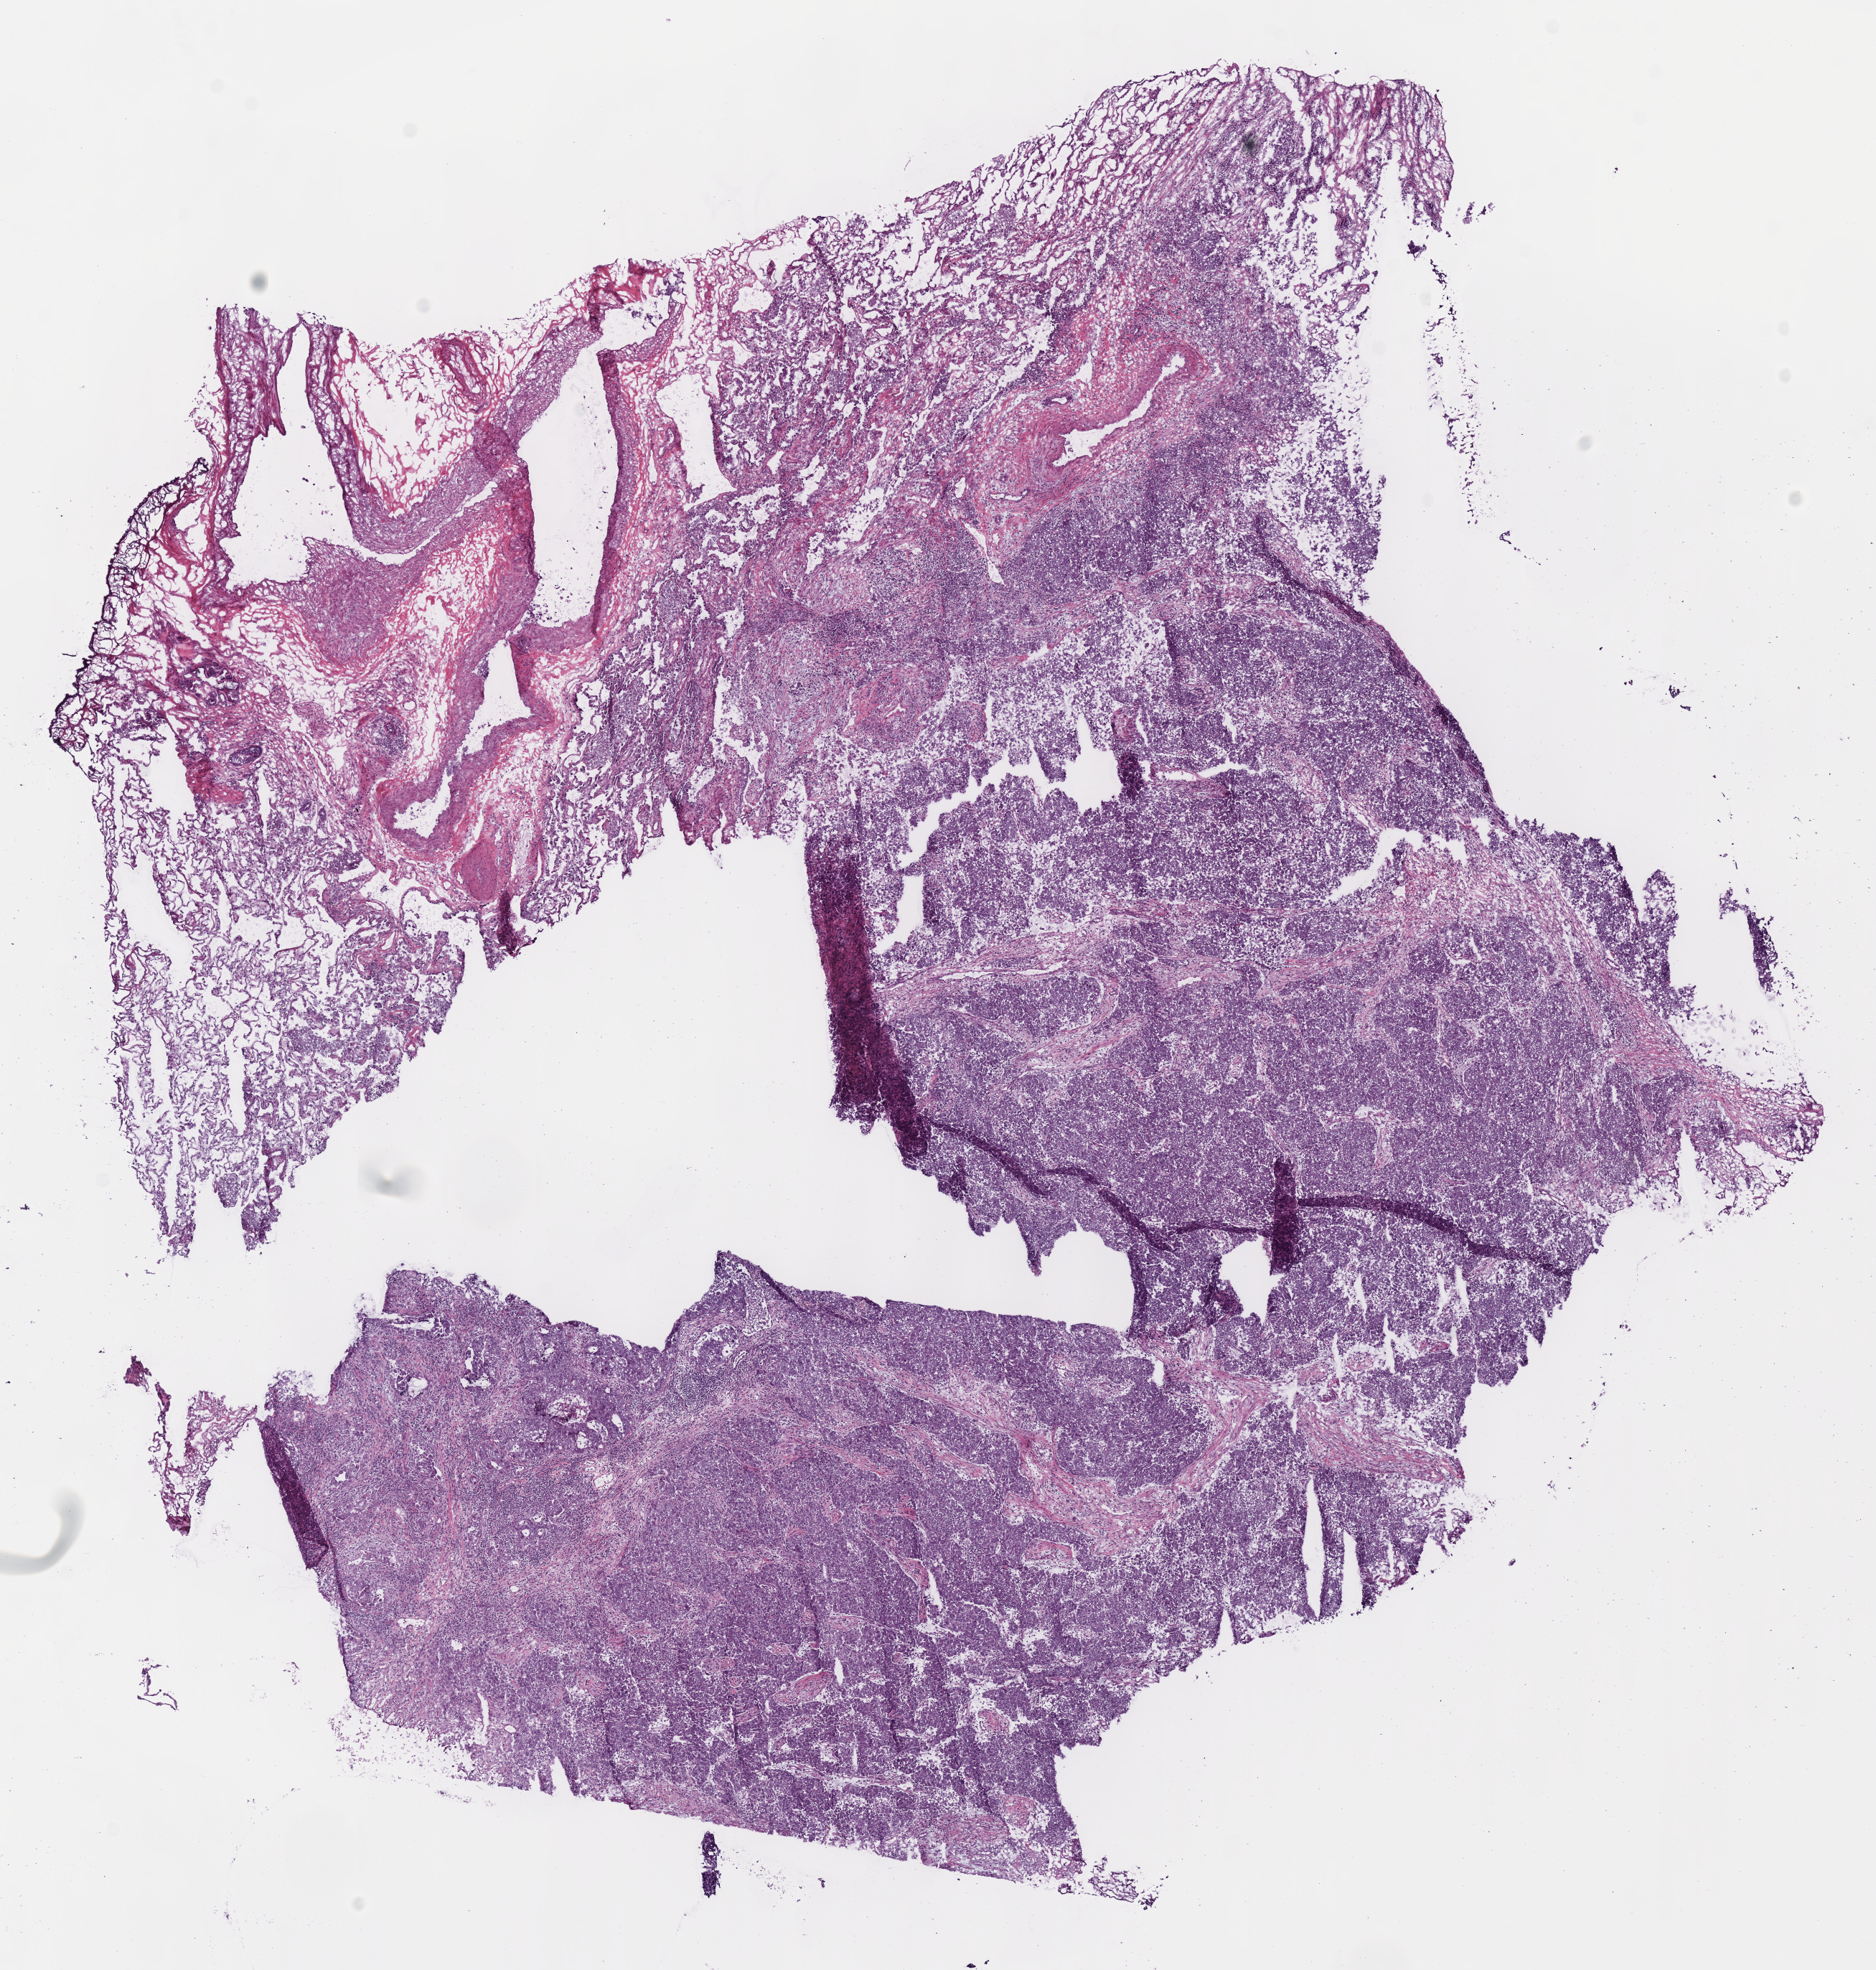
Digitized H&E tissue section (whole slide), a low-resolution overview of the entire scanned area, about 10.3 x 10.8 mm (from a 40x scan), frozen section from the bottom of the tissue portion, primary tumour sample from the lung. Female, age 68 years at initial diagnosis. Pathologist review of this section (percent, as recorded): tumour cells 55%, tumour nuclei 70%, normal cells 30%, stromal cells 10%, necrosis 5%.
- laterality: right
- AJCC pathologic stage: IB (7th edition)
- TNM: T2 N0 M0
- pathologic diagnosis: Bronchiolo-alveolar adenocarcinoma, NOS (lower lobe, lung)